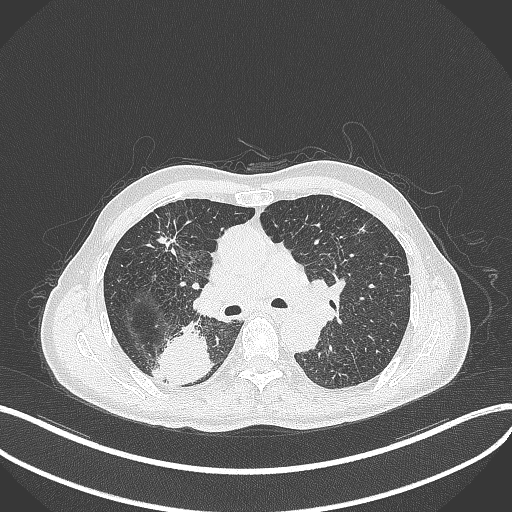
Chest CT, one axial slice; position 278 of 428 along the scan axis; lung window (W 1500 / L -600 HU); 1 mm slice thickness; 512 × 512 image matrix, field of view 400 × 400 mm. Patient: male, 79 years. Case-level facts recorded for this patient, not image findings: clinical TNM (as recorded): T3 N0 M0.
Annotated regions visible in this slice (bounding box drawn by a radiologist):
- lung tumour (recorded histology: adenocarcinoma): box from (x=156, y=319) to (x=215, y=387) px